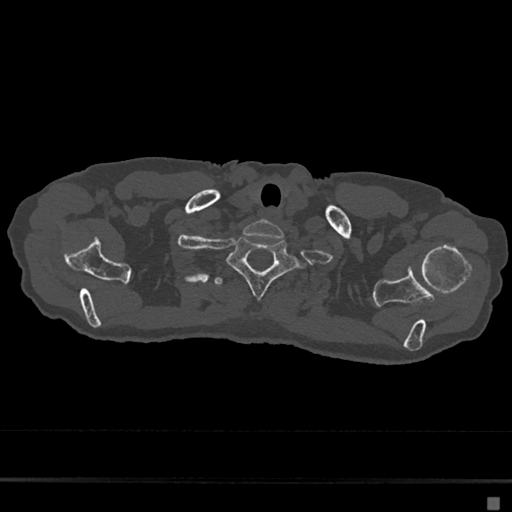
CT including the spine, one axial slice; position 608 of 797 along the scan axis; reconstruction kernel Br40s/3; bone window (W 1800 / L 400 HU); 0.5 mm slice thickness; 512 × 512 image matrix. Female patient, age 68 years. From the clinical record (not read from this slice): primary cancer: renal.
Structures marked on this image (semi-automatically segmented with operator editing):
- T1 vertebra: bounding box [x1, y1, x2, y2] px = [227, 236, 297, 299]
- T2 vertebra: [214, 277, 297, 289]